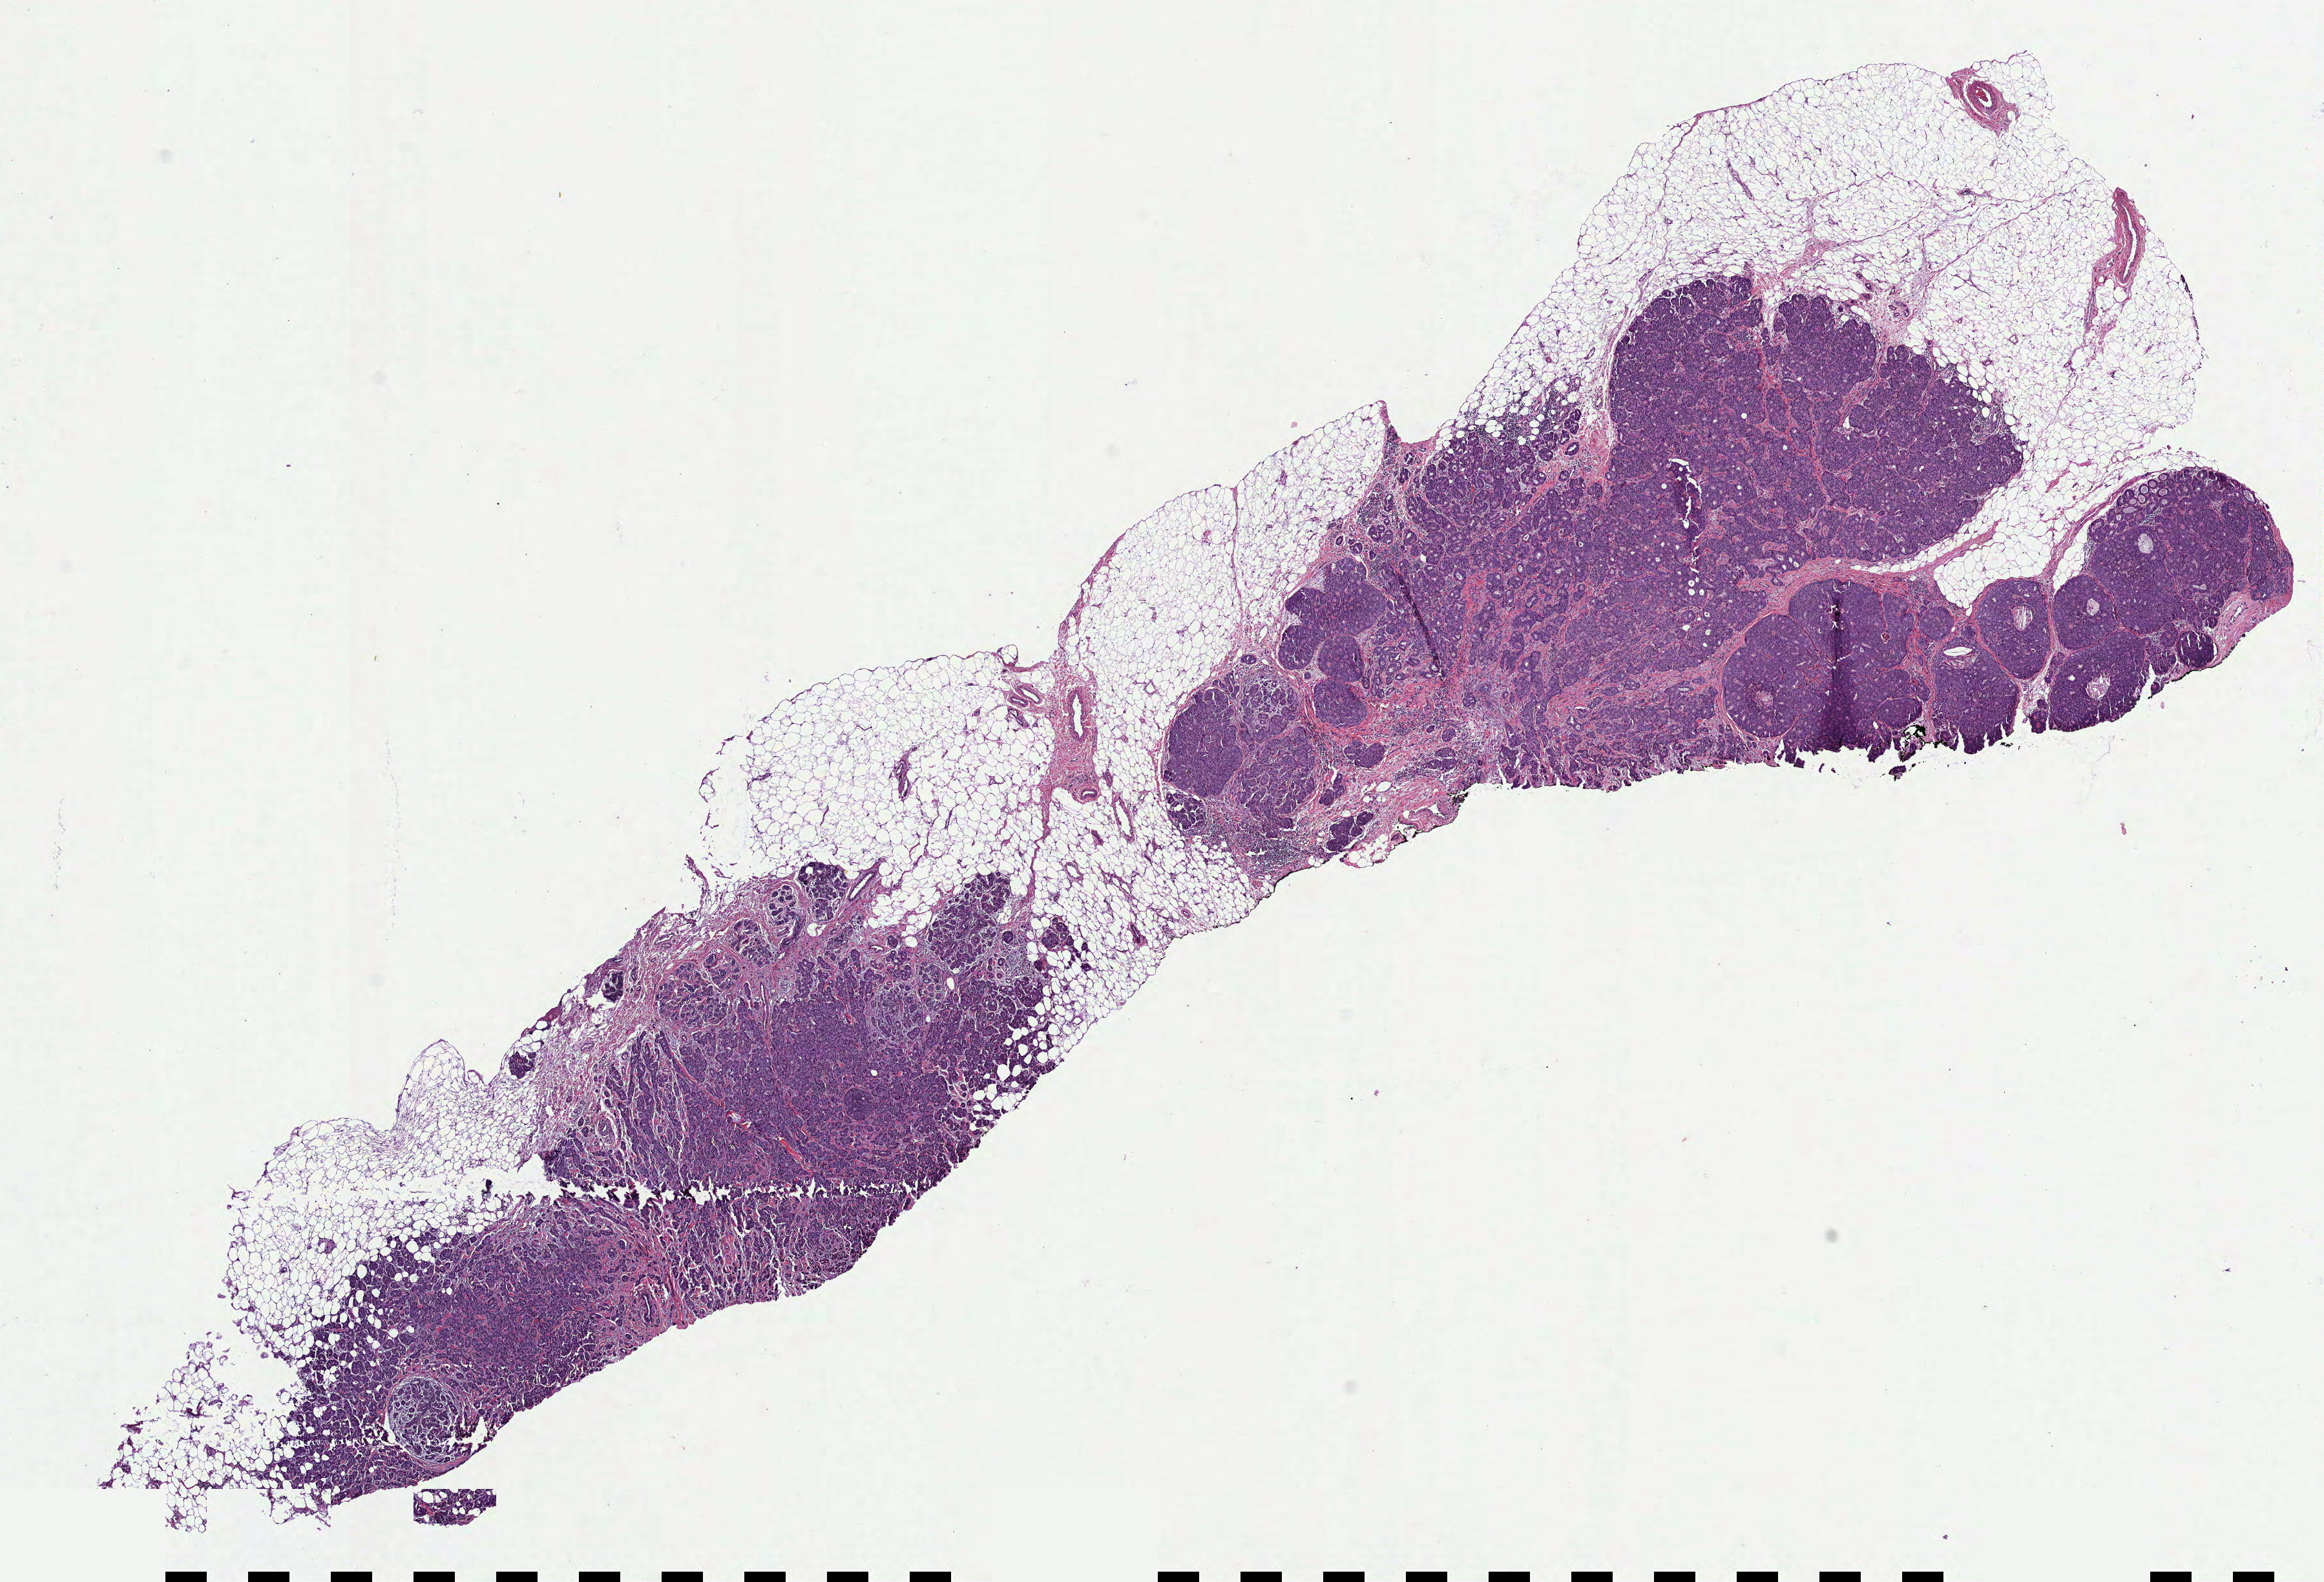
Whole-slide histology image, H&E, low-resolution overview of the scanned area, about 14.5 x 9.9 mm. Formalin-fixed paraffin-embedded (FFPE) diagnostic section. Breast, primary tumour sample. Female, age 43 years at initial diagnosis.
• TNM: T2 N1a MX
• AJCC pathologic stage: IIB
• lymph nodes positive (case pathology): 2 of 16 examined
• histologic diagnosis: Infiltrating duct carcinoma, NOS